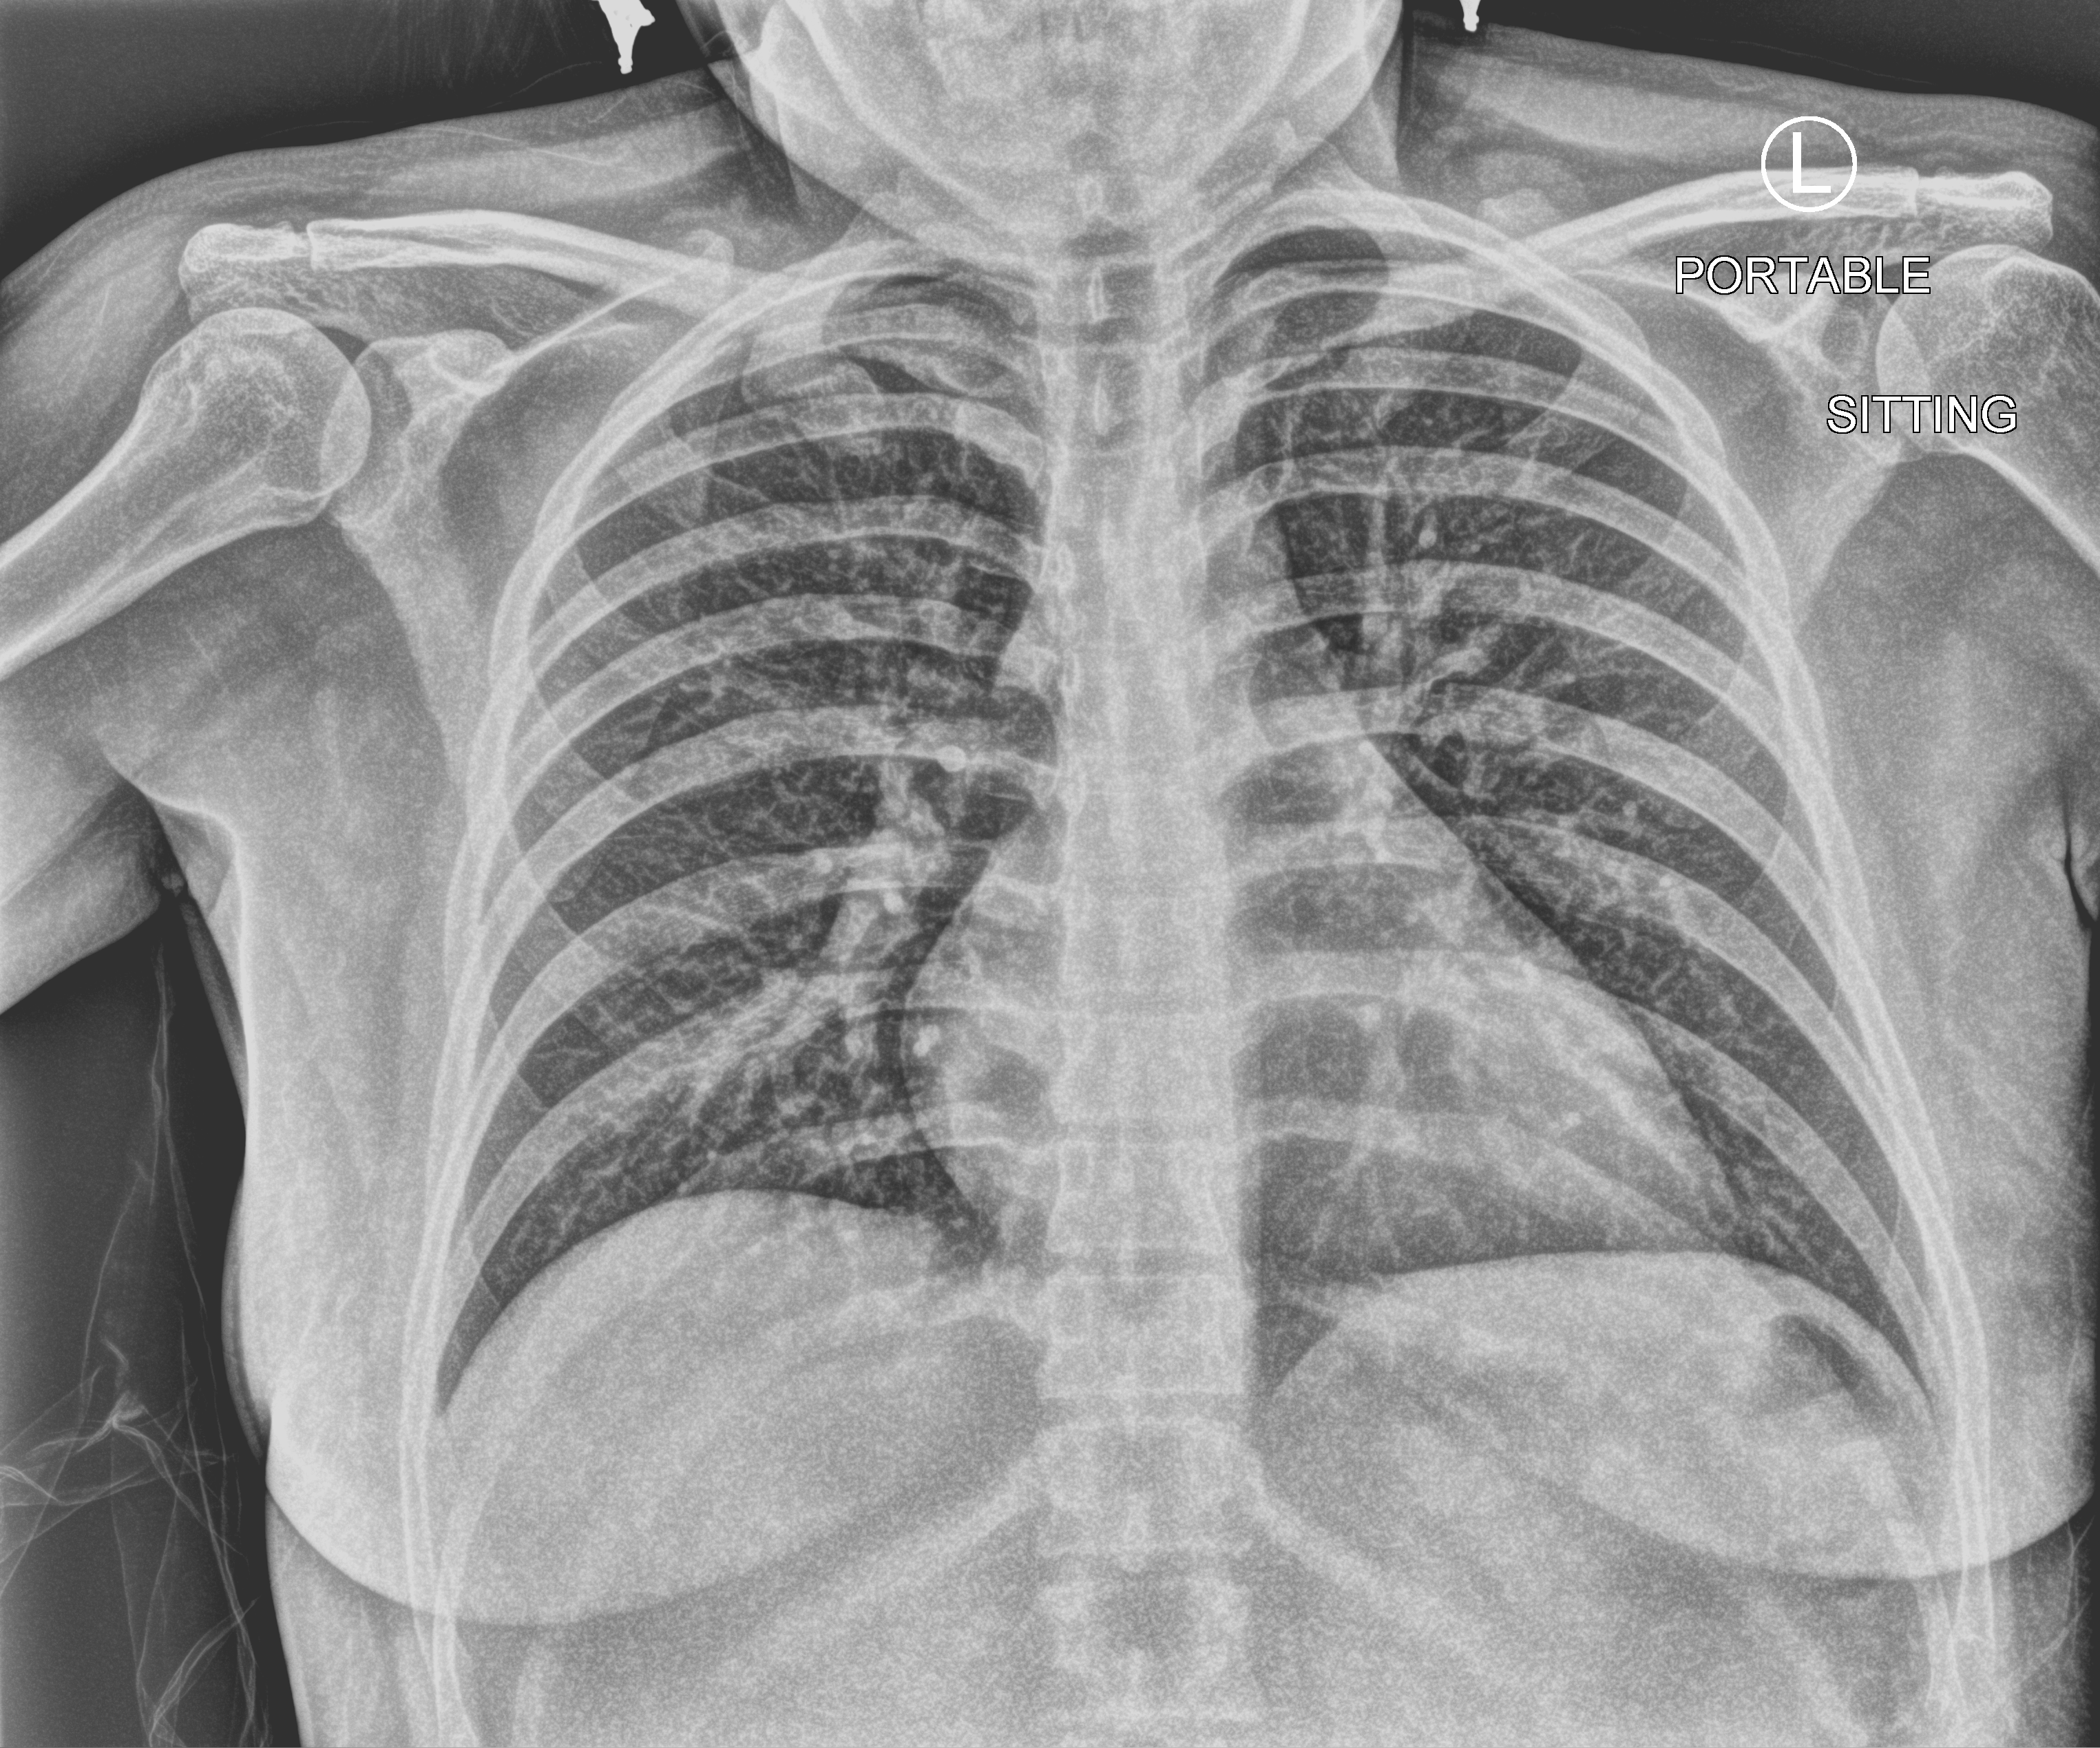
Bedside chest radiograph (computed radiography); anteroposterior (AP) projection. Patient hospitalised with COVID-19; female, aged 18–59 years.
From the hospital-stay record, not from the radiograph (when in the stay this image was taken is not recorded): COPD (admission record): no.